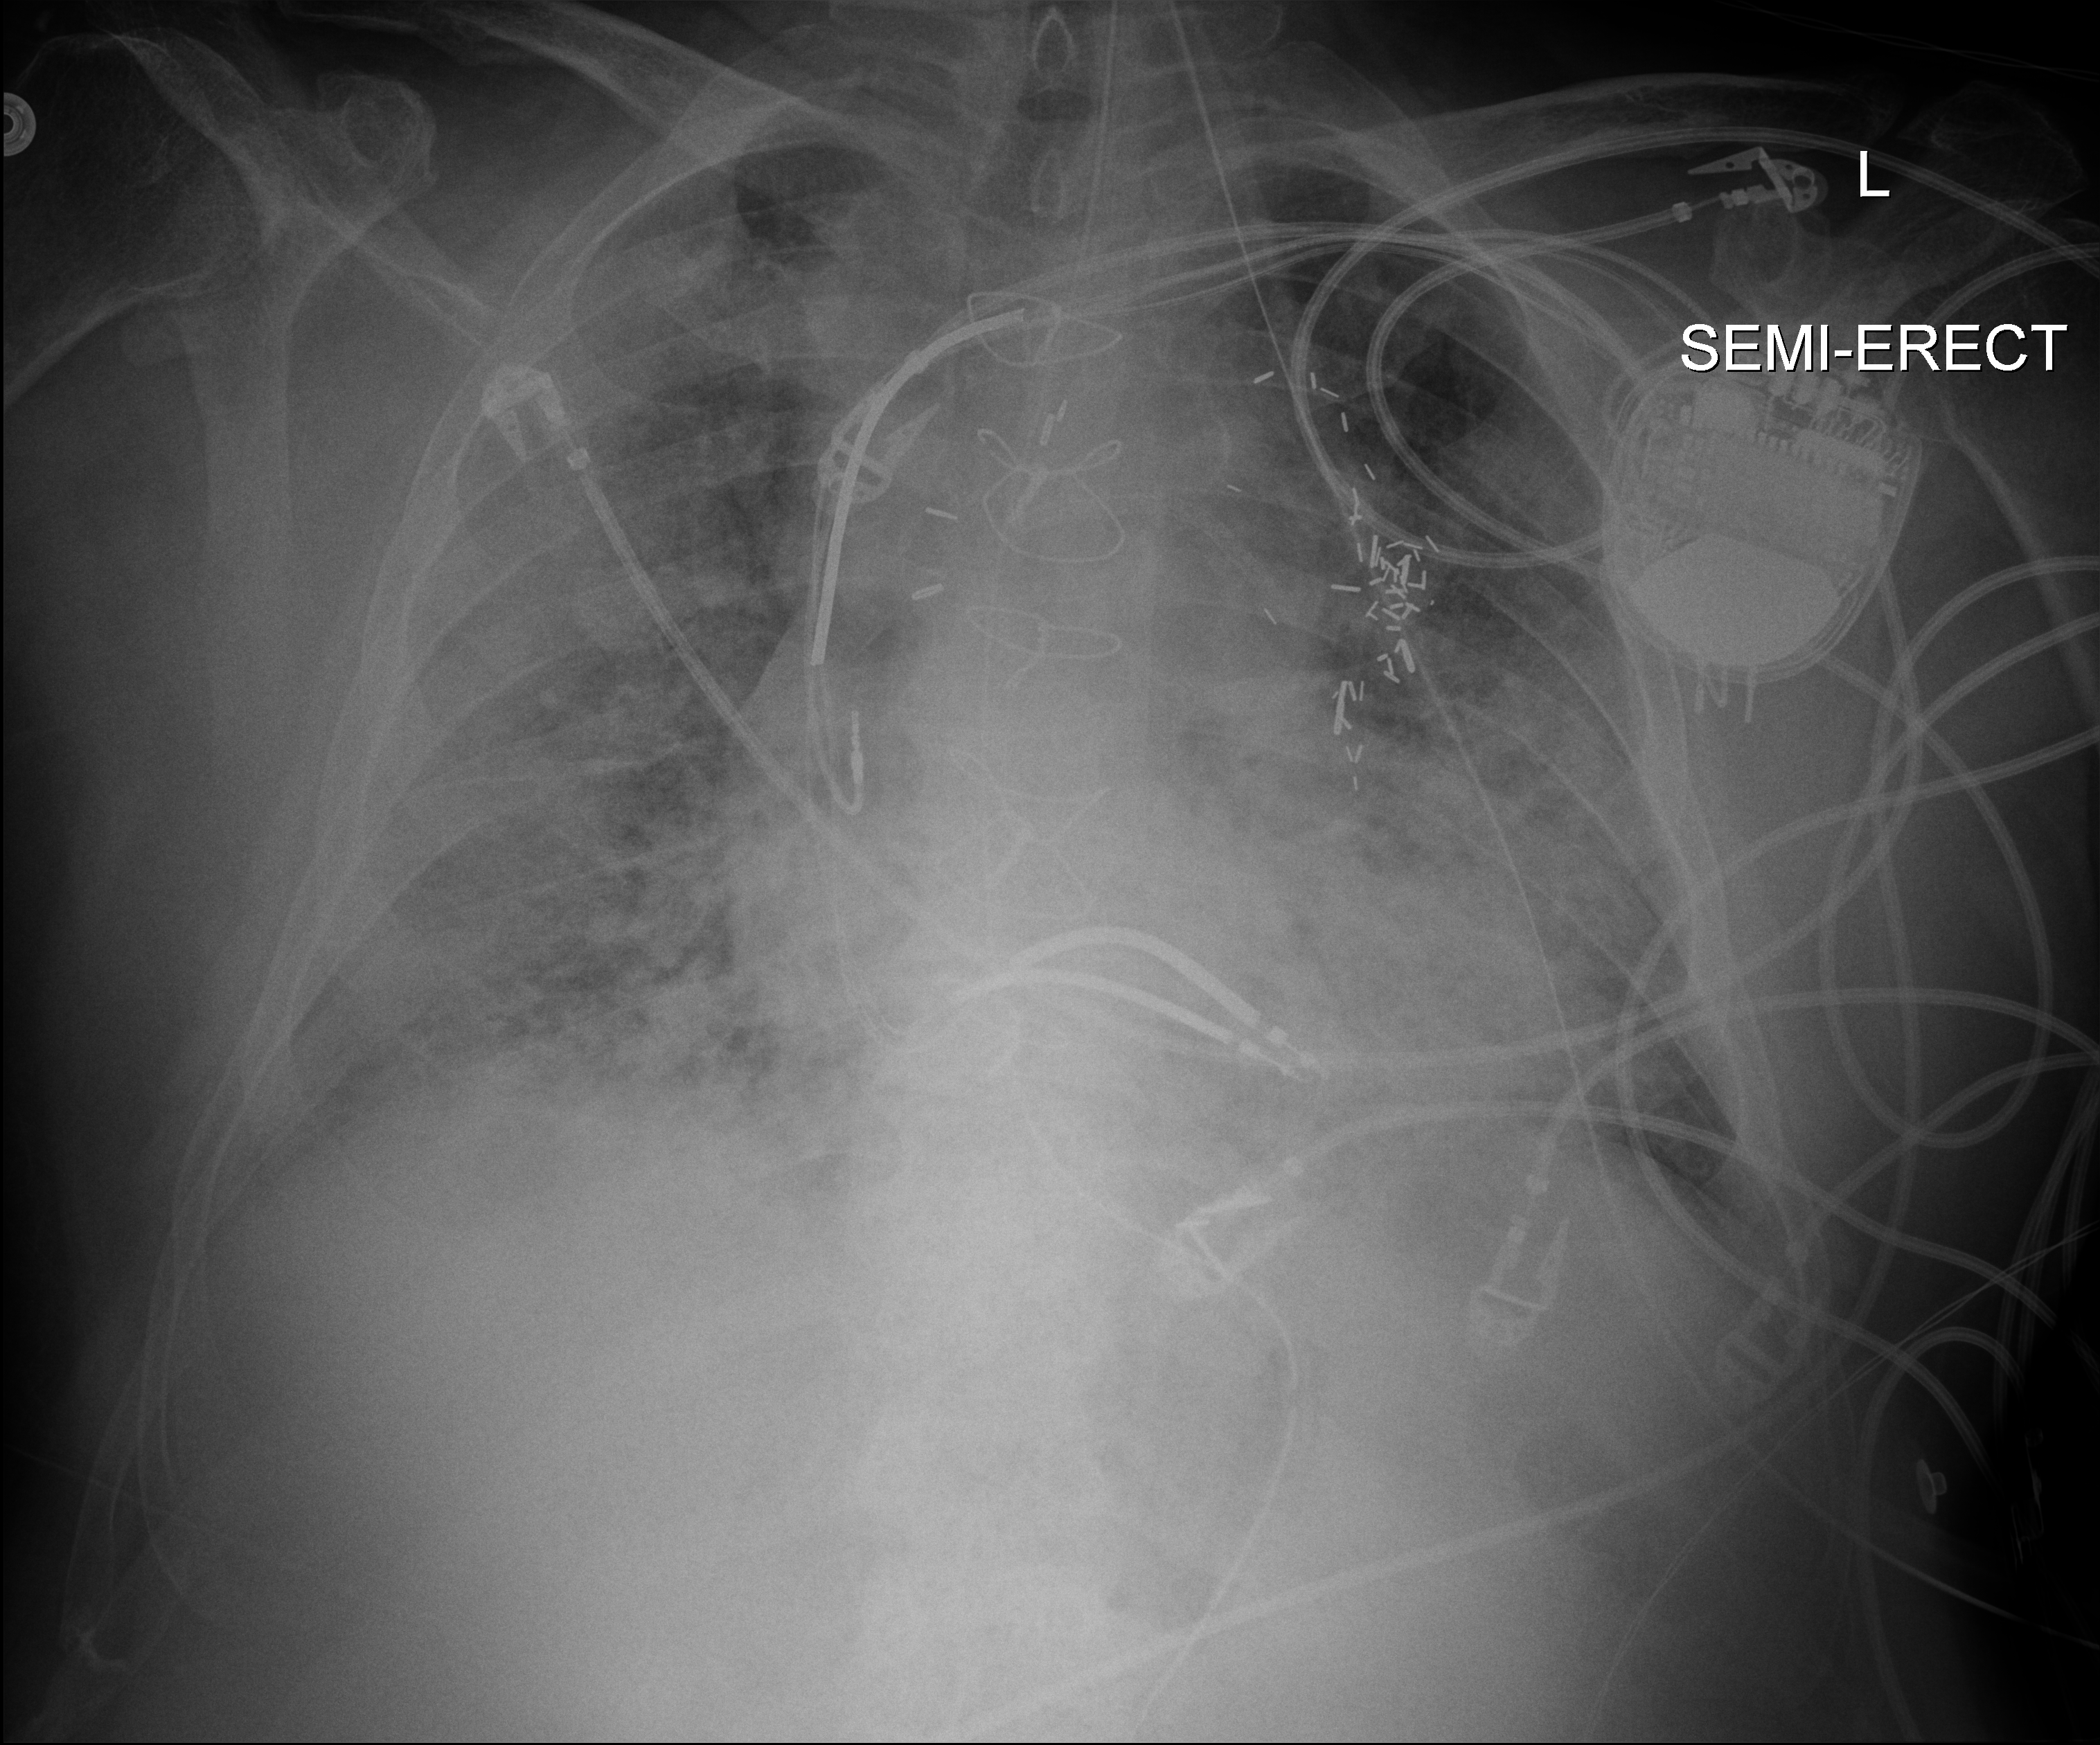
Chest X-ray (portable), anteroposterior (AP) projection. Patient hospitalised with COVID-19; male, aged 60–74 years.
Hospital-stay facts (about this admission, not read from this image; timing relative to this image not recorded):
- diabetes (admission record): yes
- admitted to intensive care during this hospital stay: yes
- mechanically ventilated during this hospital stay: yes